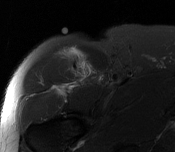
MRI of an extremity soft-tissue mass, one axial slice; slice 115 of 116 in the series (ordered by position); T2-weighted fat-saturated; MR volume resampled by the dataset authors to the PET/CT grid (not the native acquisition matrix); 3.27 mm slice thickness; 175 × 152 image matrix. Male patient. From the clinical record (not read from this slice): histological type: pleiomorphic leiomyosarcoma; grade: intermediate; site of the primary tumour: right thigh.
Annotated regions visible in this slice (expert contour drawn on MRI and transferred to this co-registered scan by the dataset authors):
- gross tumour volume including surrounding oedema: bounding box <76,61,89,75> (left, top, right, bottom; pixels)